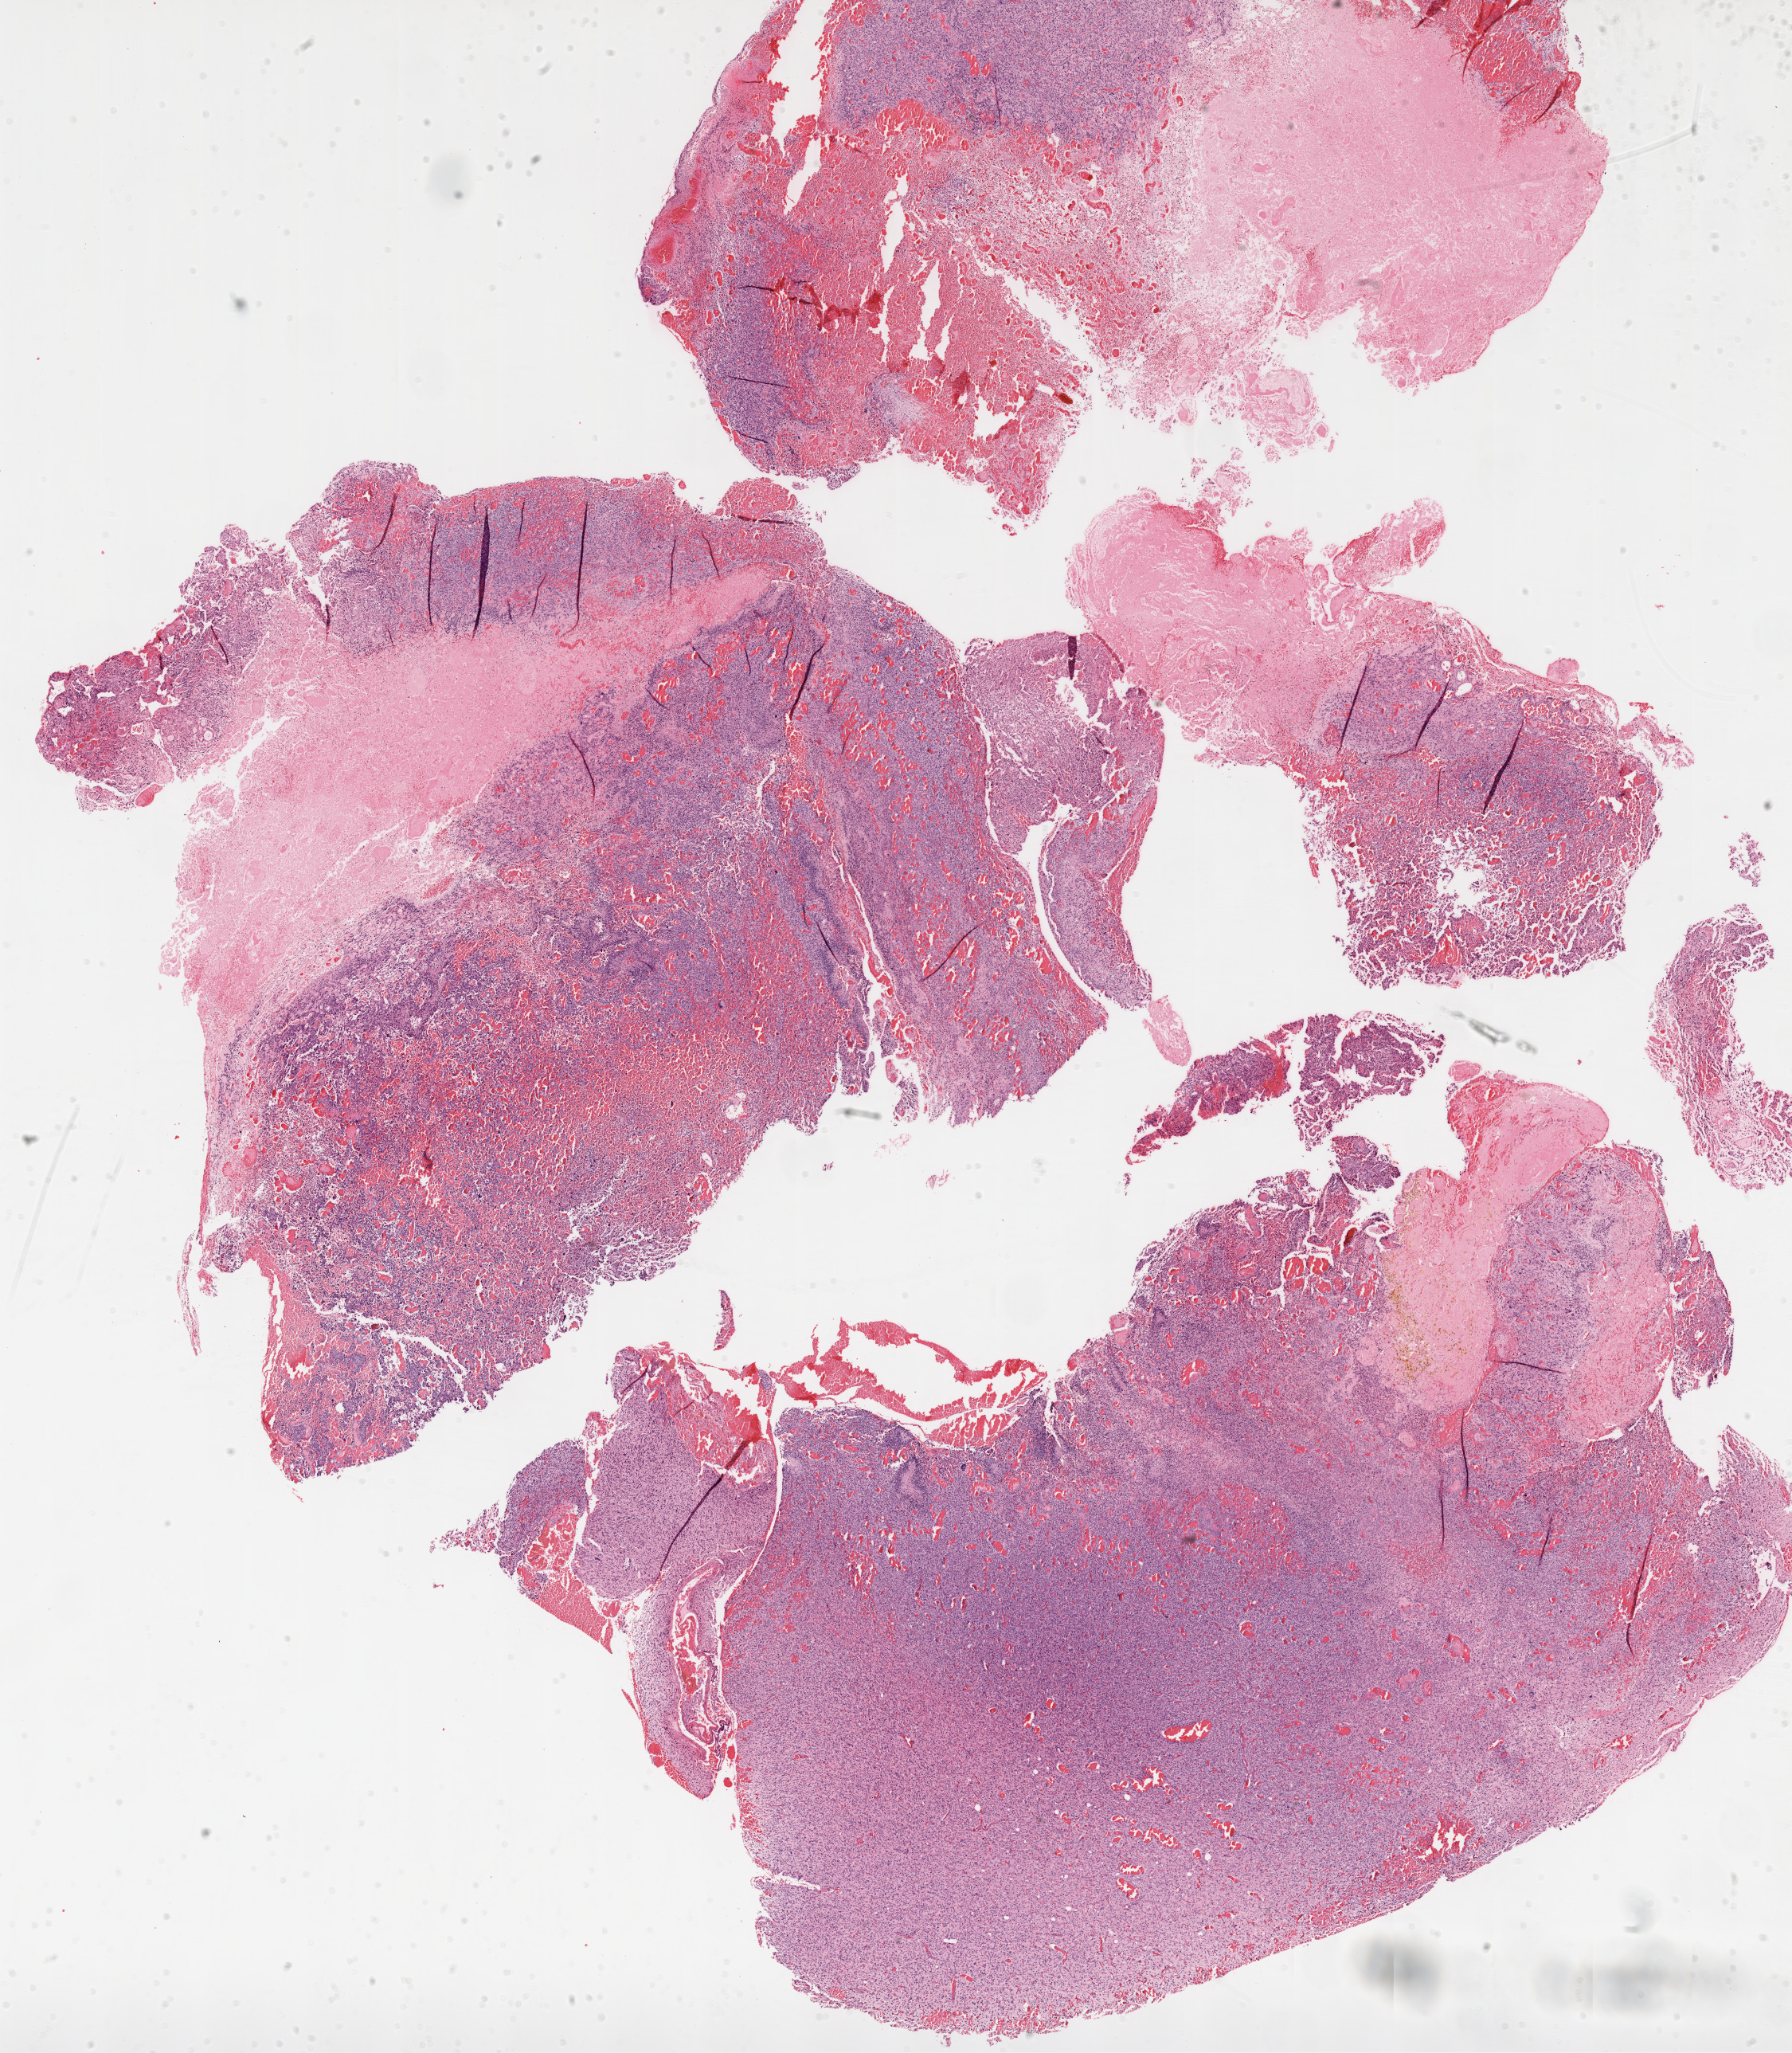
H&E whole-slide image — whole scanned area (about 18.1 x 20.7 mm, from a 20x scan) shown as a low-resolution overview, formalin-fixed paraffin-embedded (FFPE) diagnostic section, brain, primary tumour sample. Patient: female, age at initial diagnosis 36 years.
- pathologic diagnosis: Glioblastoma